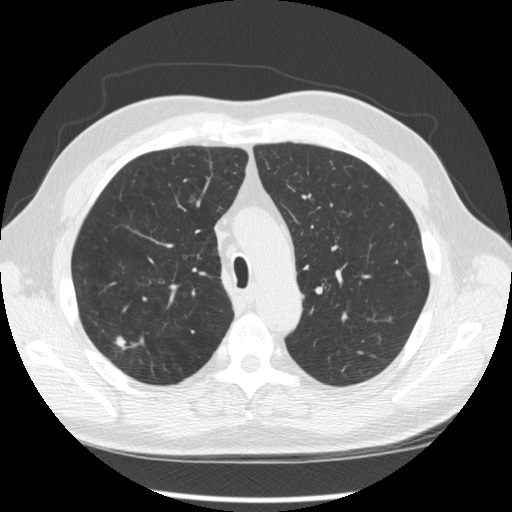
Low-dose screening chest CT, axial slice, second screening round (one year after baseline), lung window (W 1500 / L -600 HU), 2.5 mm slice thickness, 120 kVp, slice 79 of 289 in the series. Male, age 64 years at enrolment. Former smoker at enrolment.
- Expert-annotated lung lesion, bounding box <106,325,150,366> (left, top, right, bottom; pixels).
- The screening reader recorded 3 non-calcified nodules or masses ≥4 mm on this exam (right upper lobe, right upper lobe, right upper lobe); which of them this box marks is not recorded.
- Official screen result: positive, other.
- Later outcome: lung cancer diagnosed 411 days after this screen — adenocarcinoma, NOS, right upper lobe, moderately differentiated (G2), stage IA (AJCC 6th edition), 14 mm at pathology.